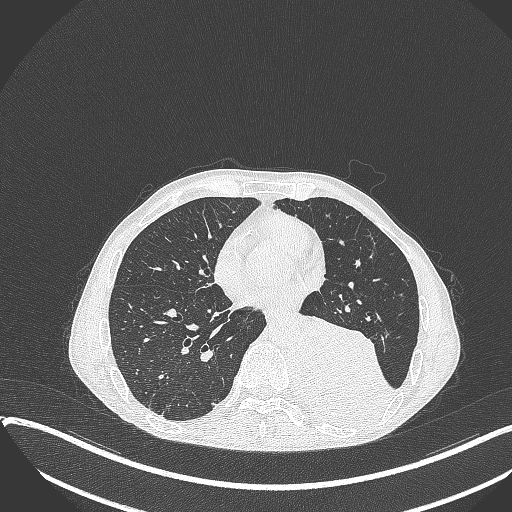
Chest CT, one axial slice. Position 148 of 401 along the scan axis. Lung window (W 1500 / L -600 HU). 1 mm slice thickness. 512 × 512 image matrix, field of view 400 × 400 mm. Male patient, age 57 years. From the clinical record (not read from this slice): clinical TNM (as recorded): T4 N0 M0.
Structures marked on this image (bounding box drawn by a radiologist):
- lung tumour (recorded histology: squamous cell carcinoma): box from (x=291, y=305) to (x=397, y=435) px